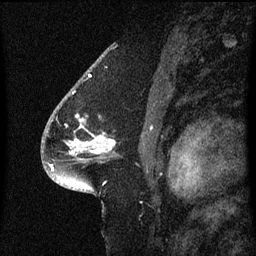
Breast MRI (dynamic contrast-enhanced), one sagittal slice. Position 41 of 60 along the scan axis. Dynamic contrast-enhanced series, image 2 of 3 at this slice position (ordered by acquisition). 1.5 T. TE 4.2 ms, TR 8.4 ms. 2 mm slice thickness. 256 × 256 image matrix. Female patient, age 54 years. Case-level facts recorded for this patient, not image findings: setting: breast cancer imaged before/during neoadjuvant chemotherapy; receptor status: HR-positive, HER2-negative.
Outlined on this slice (semi-automatically segmented with operator editing):
- analysis volume of interest (the breast-tissue region the enhancement analysis was run in; not a lesion): bounding box (x1, y1, x2, y2) in pixels: (48, 104, 114, 165)
- tumour enhancement mask (voxels above the 70 % enhancement threshold inside the analysis volume of interest): (73, 136, 114, 153)